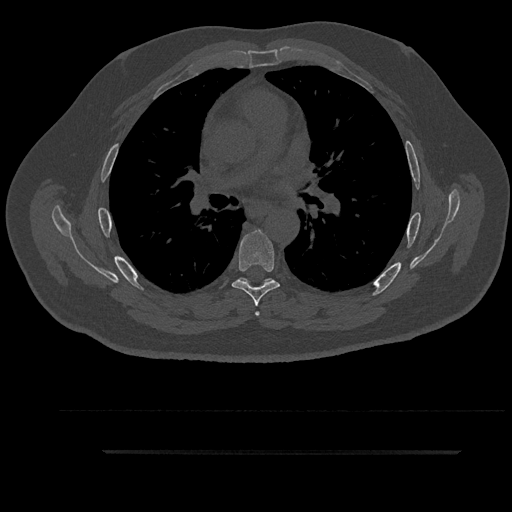
CT including the spine, one axial slice. Reconstruction kernel Br40s/3. 120 kVp. Bone window (W 1800 / L 400 HU). 0.5 mm slice thickness. 512 × 512 image matrix, field of view 432 × 432 mm. Patient: male, 63 years. From the clinical record (not read from this slice): primary cancer: renal; vertebrae with lytic lesions (as recorded): T8.
Structures marked on this image (semi-automatic segmentation, software-assisted and operator-edited):
- T5 vertebra: bounding box <237,278,273,316> (left, top, right, bottom; pixels)
- T6 vertebra: <232,230,280,306>
- T7 vertebra: <266,280,271,282>